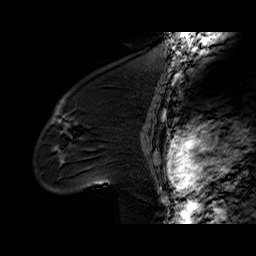
Breast MRI (dynamic contrast-enhanced), one sagittal slice. Slice 44 of 60 in the series (ordered by position). Dynamic contrast-enhanced series, time point 2 of 6 at this slice position (early post-contrast). 1.5 T. TE 6.2 ms, TR 32.4 ms. 4 mm slice thickness. 256 × 256 image matrix. Female patient. Case-level facts recorded for this patient, not image findings: setting: breast cancer imaged before/during neoadjuvant chemotherapy; receptor status: triple-negative.
Structures marked on this image (semi-automatic segmentation, software-assisted and operator-edited):
- analysis volume of interest (the breast-tissue region the enhancement analysis was run in; not a lesion): bounding box <36,97,134,194> (left, top, right, bottom; pixels)
- tumour enhancement mask (voxels above the 100 % enhancement threshold inside the analysis volume of interest): <55,101,66,125>